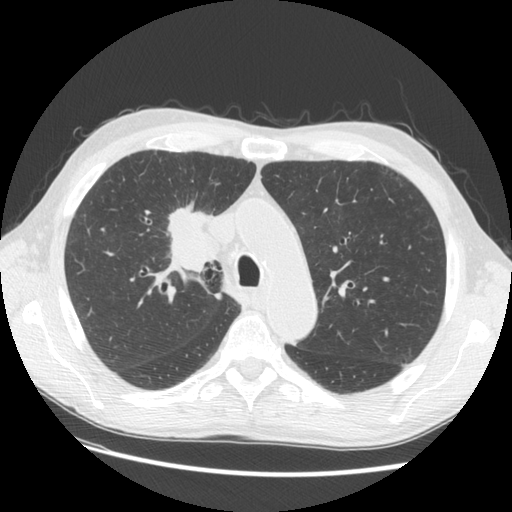
Low-dose screening chest CT, axial slice; third annual screen; lung window (W 1500 / L -600 HU); 512 × 512 image matrix, field of view 360 × 360 mm. Male participant, aged 73 years at enrolment. Current smoker at enrolment.
• Expert reader's lesion annotation, box from (x=142, y=184) to (x=234, y=278) px.
• The screening reader recorded 4 non-calcified nodules or masses ≥4 mm on this exam (right upper lobe, right upper lobe, right upper lobe, left lower lobe); which of them this box marks is not recorded.
• Participant outcome: lung cancer diagnosed 48 days after this screen — squamous cell carcinoma, NOS, right upper lobe, poorly differentiated (G3), stage IIIB (AJCC 6th edition), 56 mm at pathology.